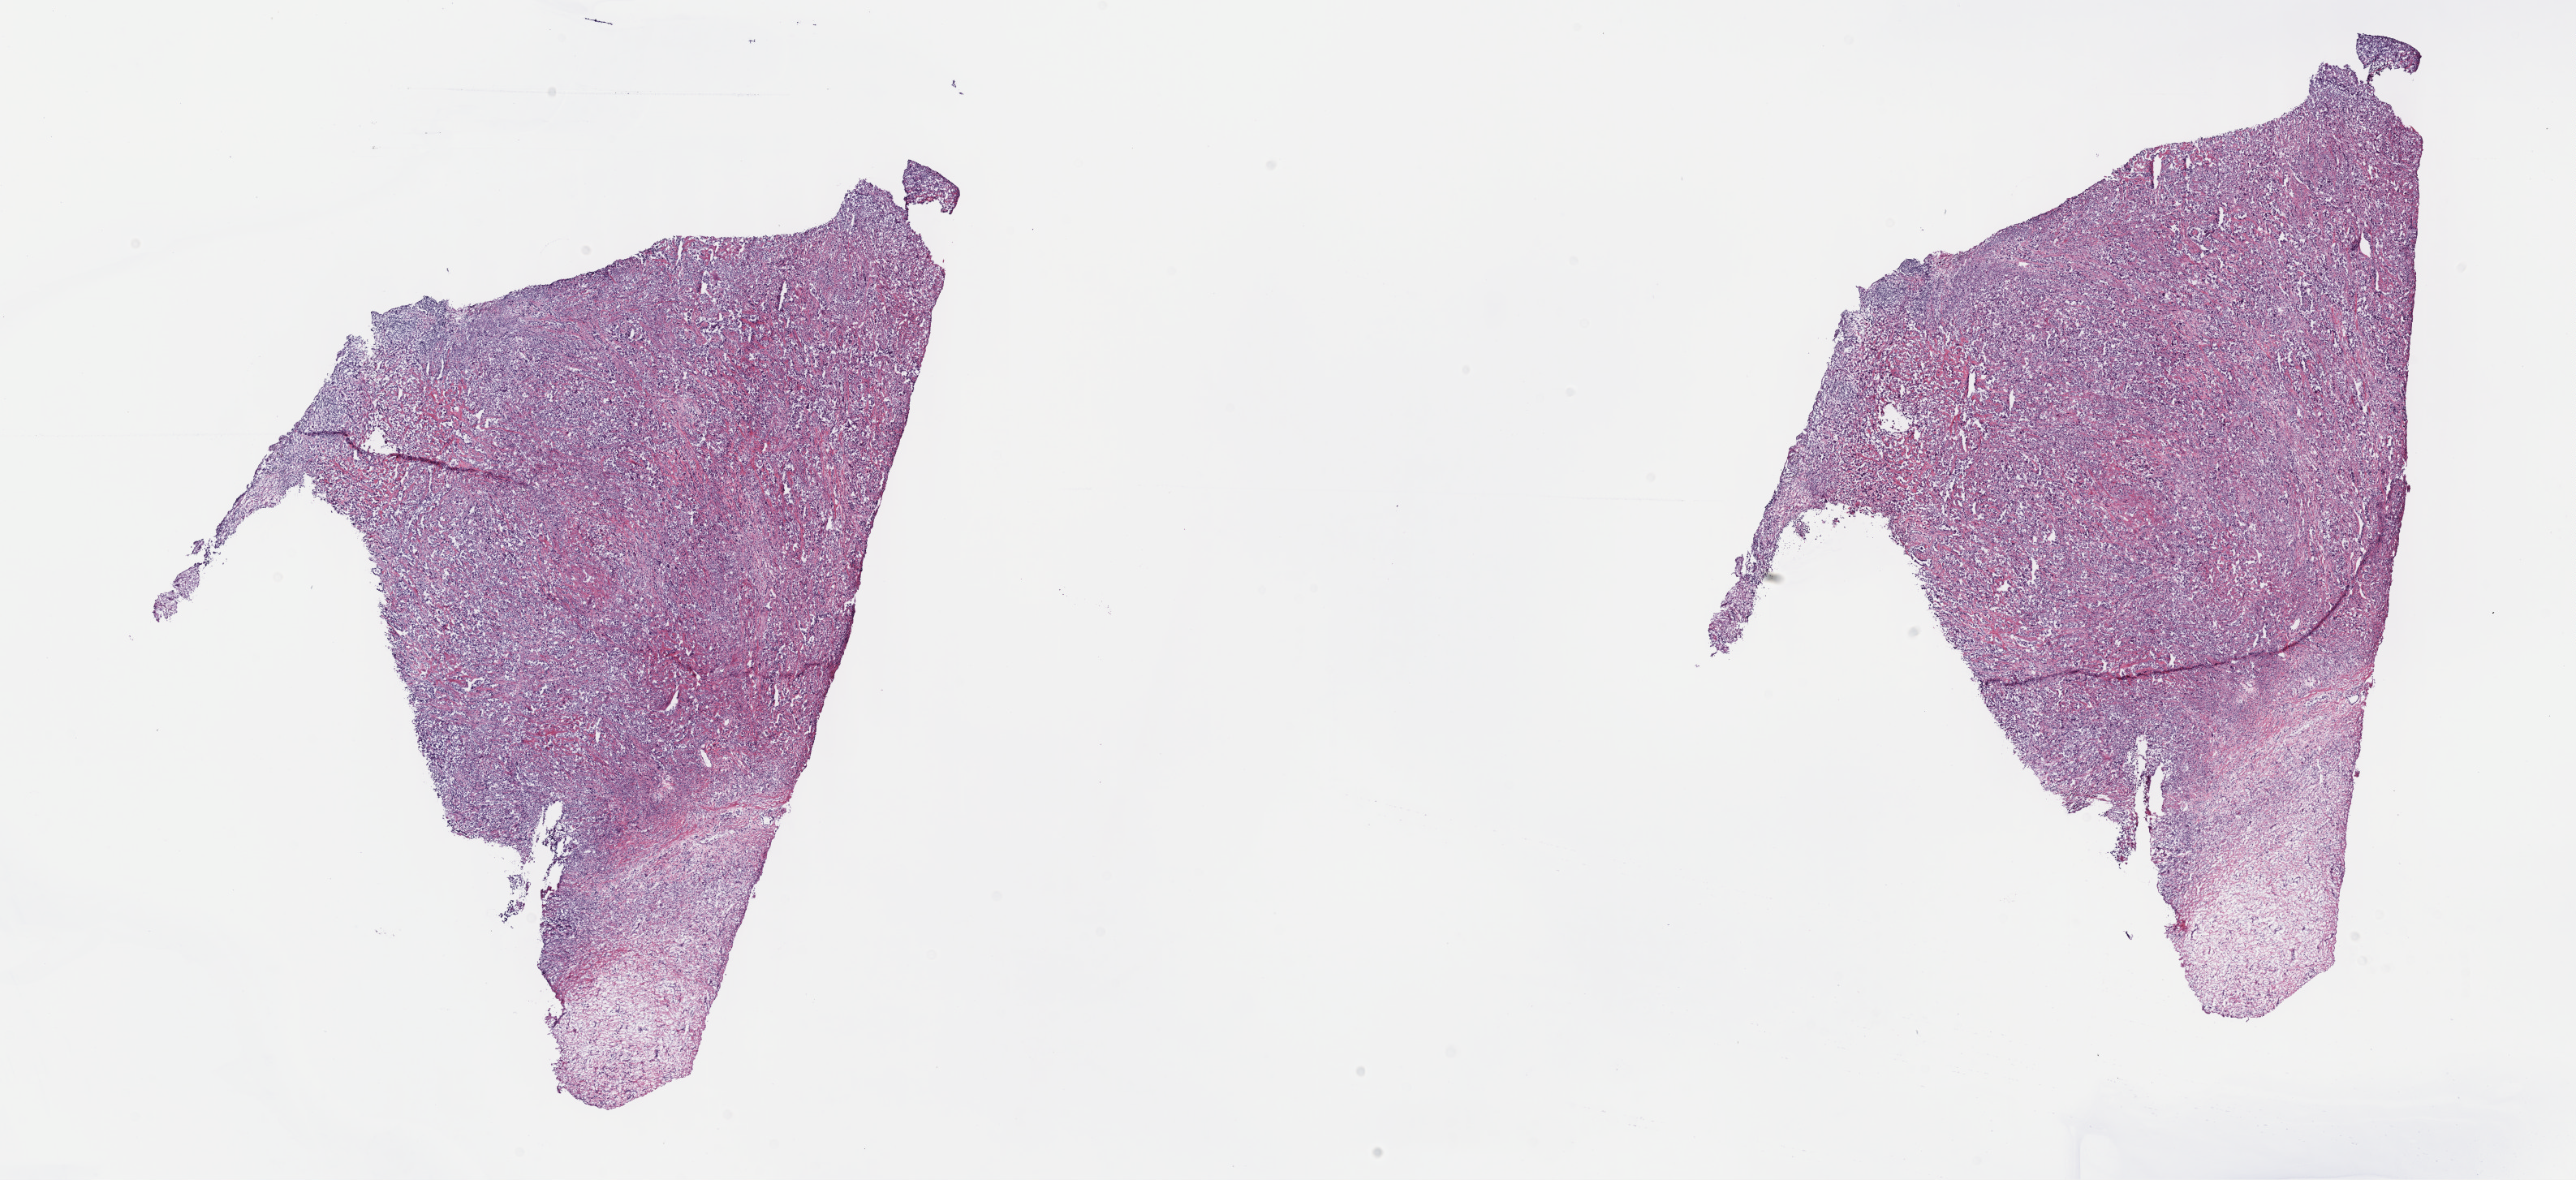
Whole-slide histology image, H&E-stained — shown as a low-resolution overview of the whole scanned area (about 25.7 x 11.8 mm), frozen section, sample: primary tumour, mesothelium. Male patient; age at initial diagnosis 55 years. Composition of this section per pathologist review: tumour cells 75%, tumour nuclei 75%, normal cells 0%, stromal cells 25%, necrosis 0%. Infiltration values recorded for this section: lymphocyte infiltration 3%, monocyte infiltration 1%, neutrophil infiltration 3%.
- diagnosis: Epithelioid mesothelioma, malignant (pleura, NOS)
- AJCC pathologic stage: III (7th edition)